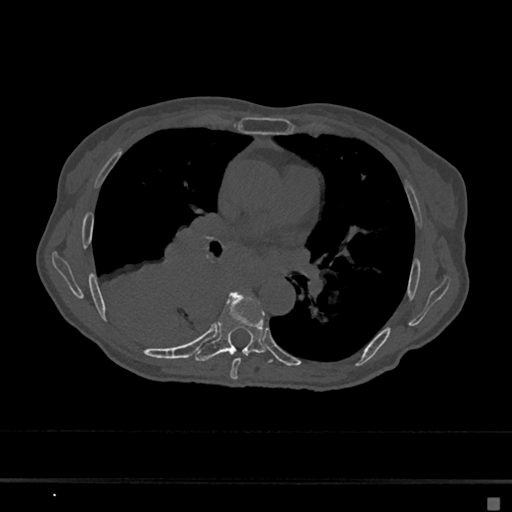
CT including the spine, one axial slice; position 389 of 797 along the scan axis; reconstruction kernel Br40s/3; 120 kVp; bone window (W 1800 / L 400 HU); 0.5 mm slice thickness; 512 × 512 image matrix, field of view 360 × 360 mm. Patient: female, 68 years. Case-level facts recorded for this patient, not image findings: primary cancer: renal.
Outlined on this slice (semi-automatic segmentation, software-assisted and operator-edited):
- T6 vertebra: box from (x=230, y=310) to (x=264, y=380) px
- T7 vertebra: (x=195, y=292)–(x=273, y=363)